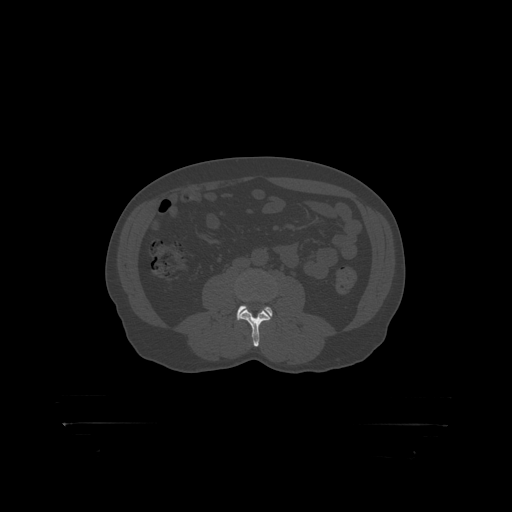
CT including the spine, one axial slice; slice 255 of 399 in the series (ordered by position); reconstruction kernel STANDARD; 120 kVp; bone window (W 1800 / L 400 HU); 512 × 512 image matrix, field of view 650 × 650 mm. Male patient, age 46 years. Case-level facts recorded for this patient, not image findings: primary cancer: skin.
Structures marked on this image (semi-automatic segmentation, software-assisted and operator-edited):
- L3 vertebra: bounding box (x1, y1, x2, y2) in pixels: (240, 298, 270, 319)
- L4 vertebra: (237, 306, 273, 317)